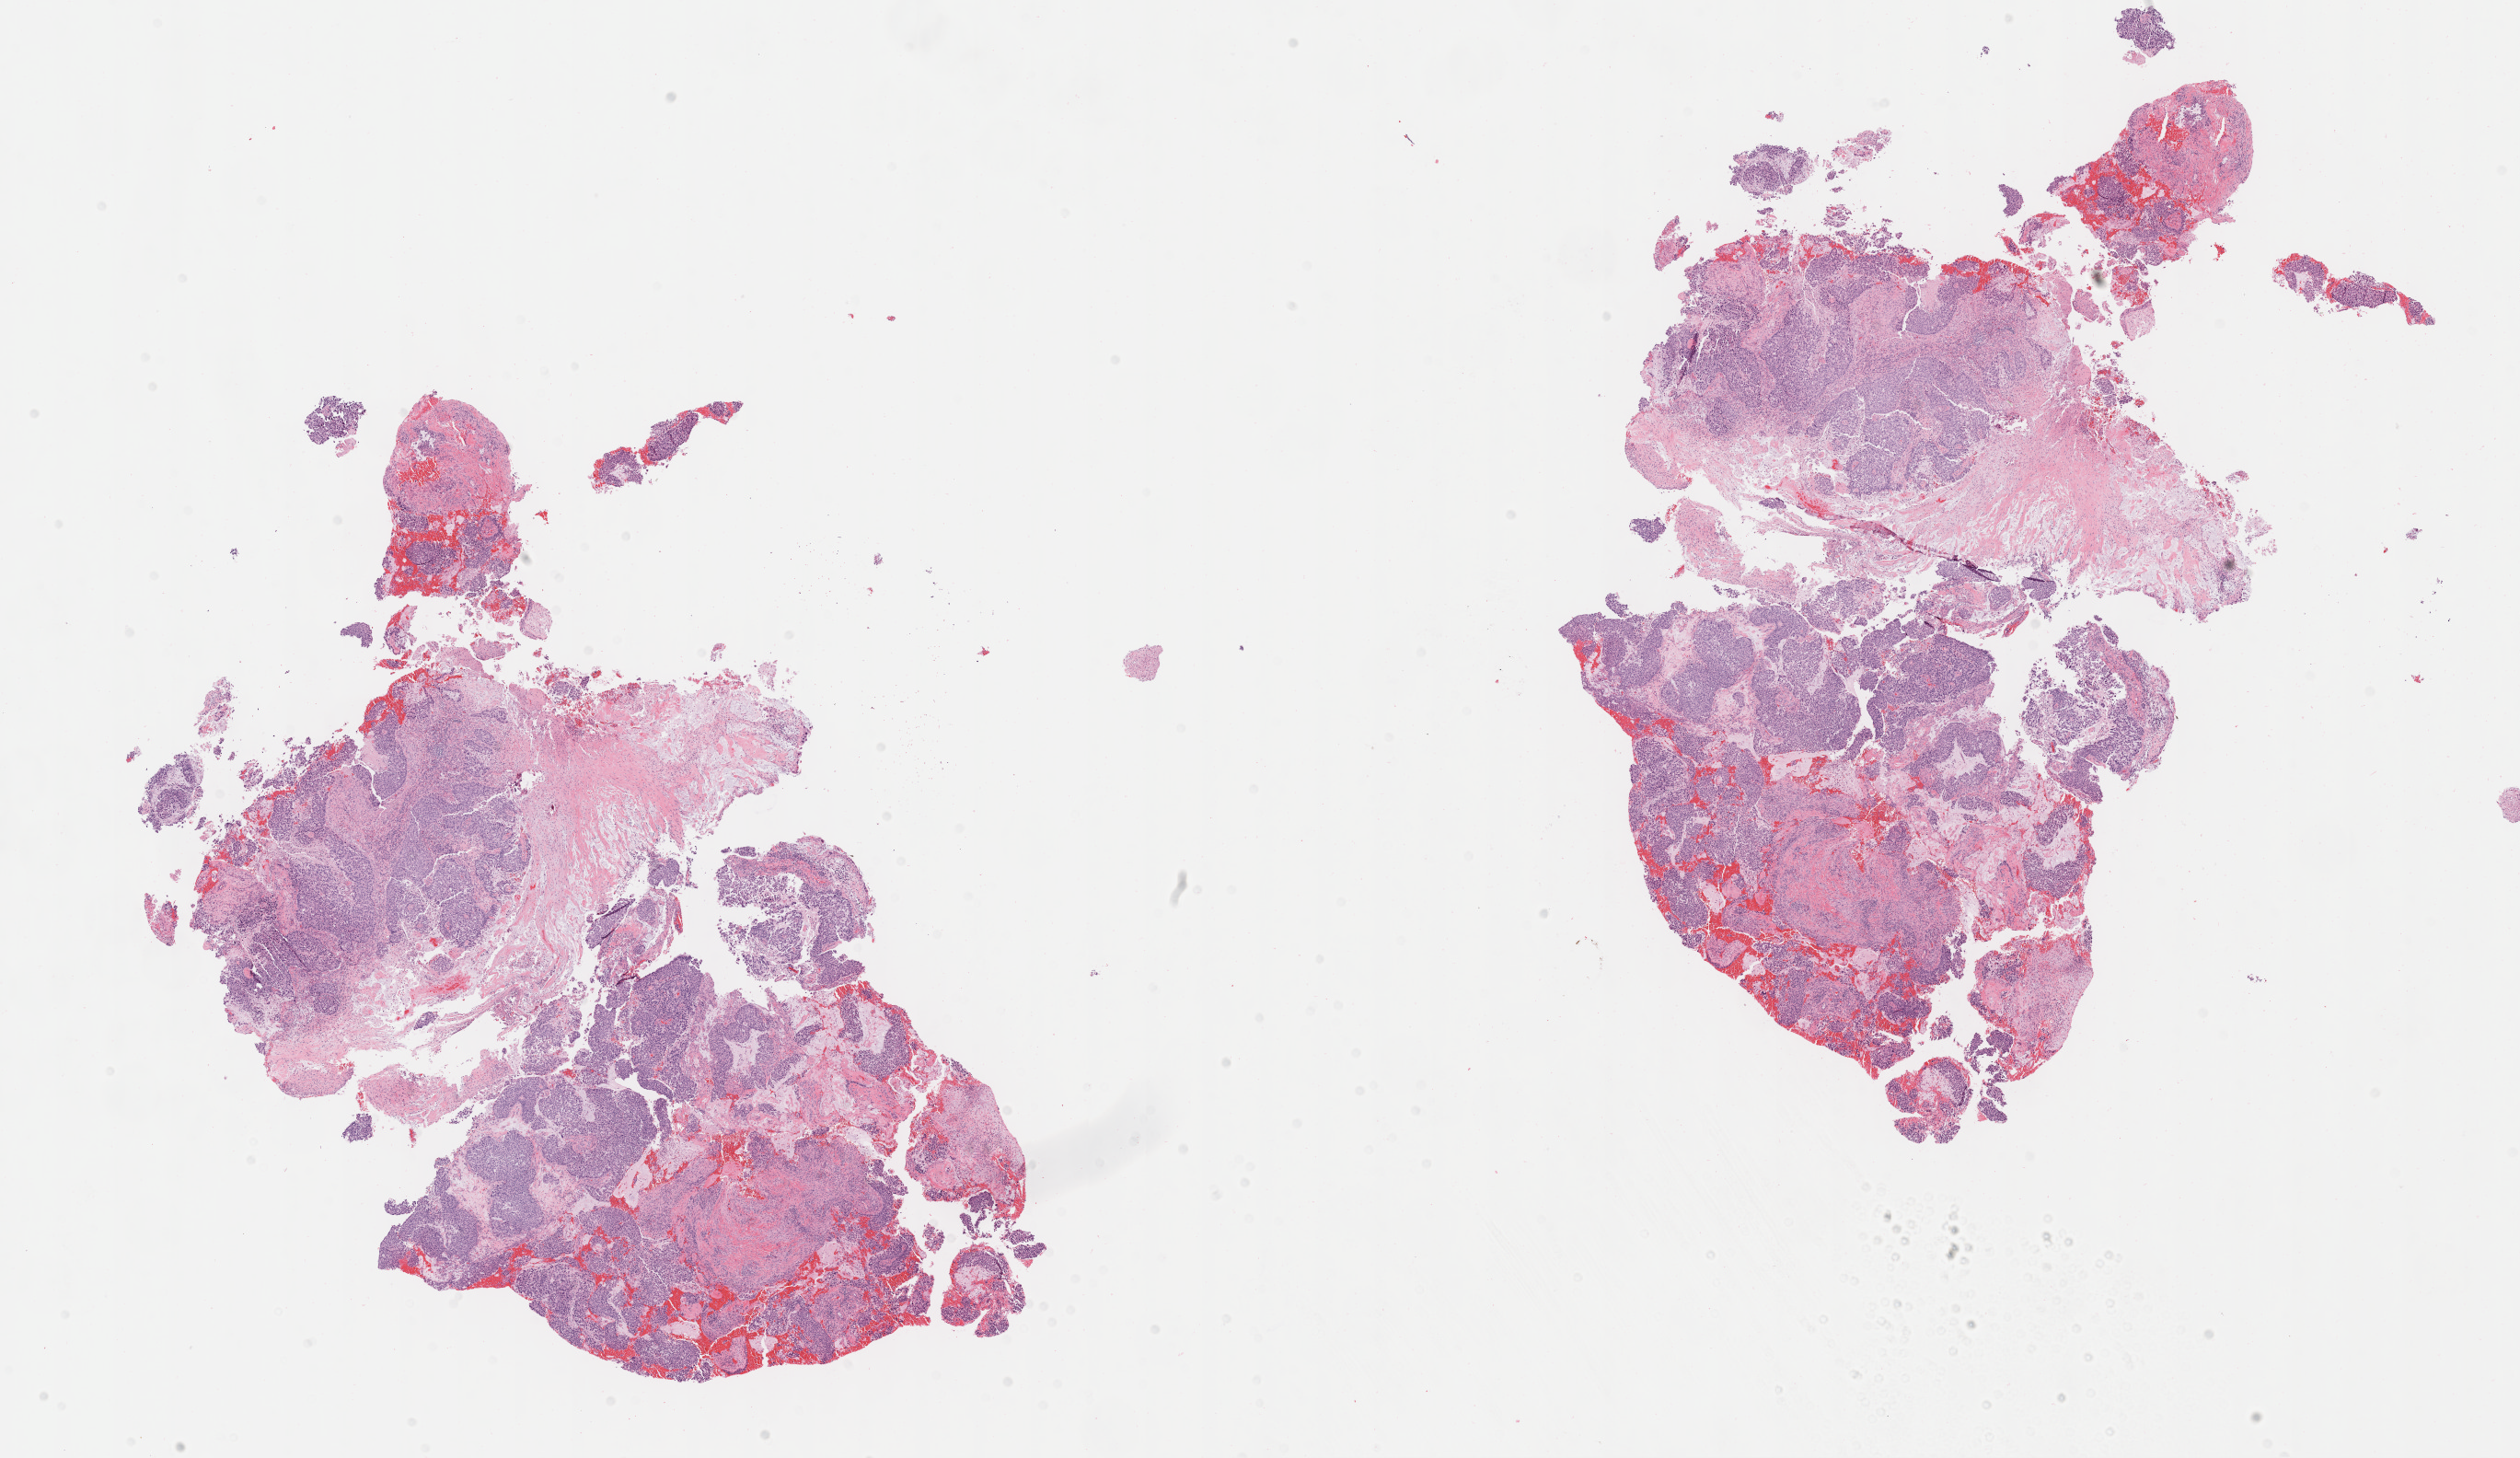
Whole-slide image, H&E stain, a low-resolution overview of the entire scanned area, about 22.1 x 12.8 mm, tumor tissue, site: cervix. Patient: female, aged 69.
Histologic diagnosis: Squamous cell carcinoma, large cell, nonkeratinizing, NOS.